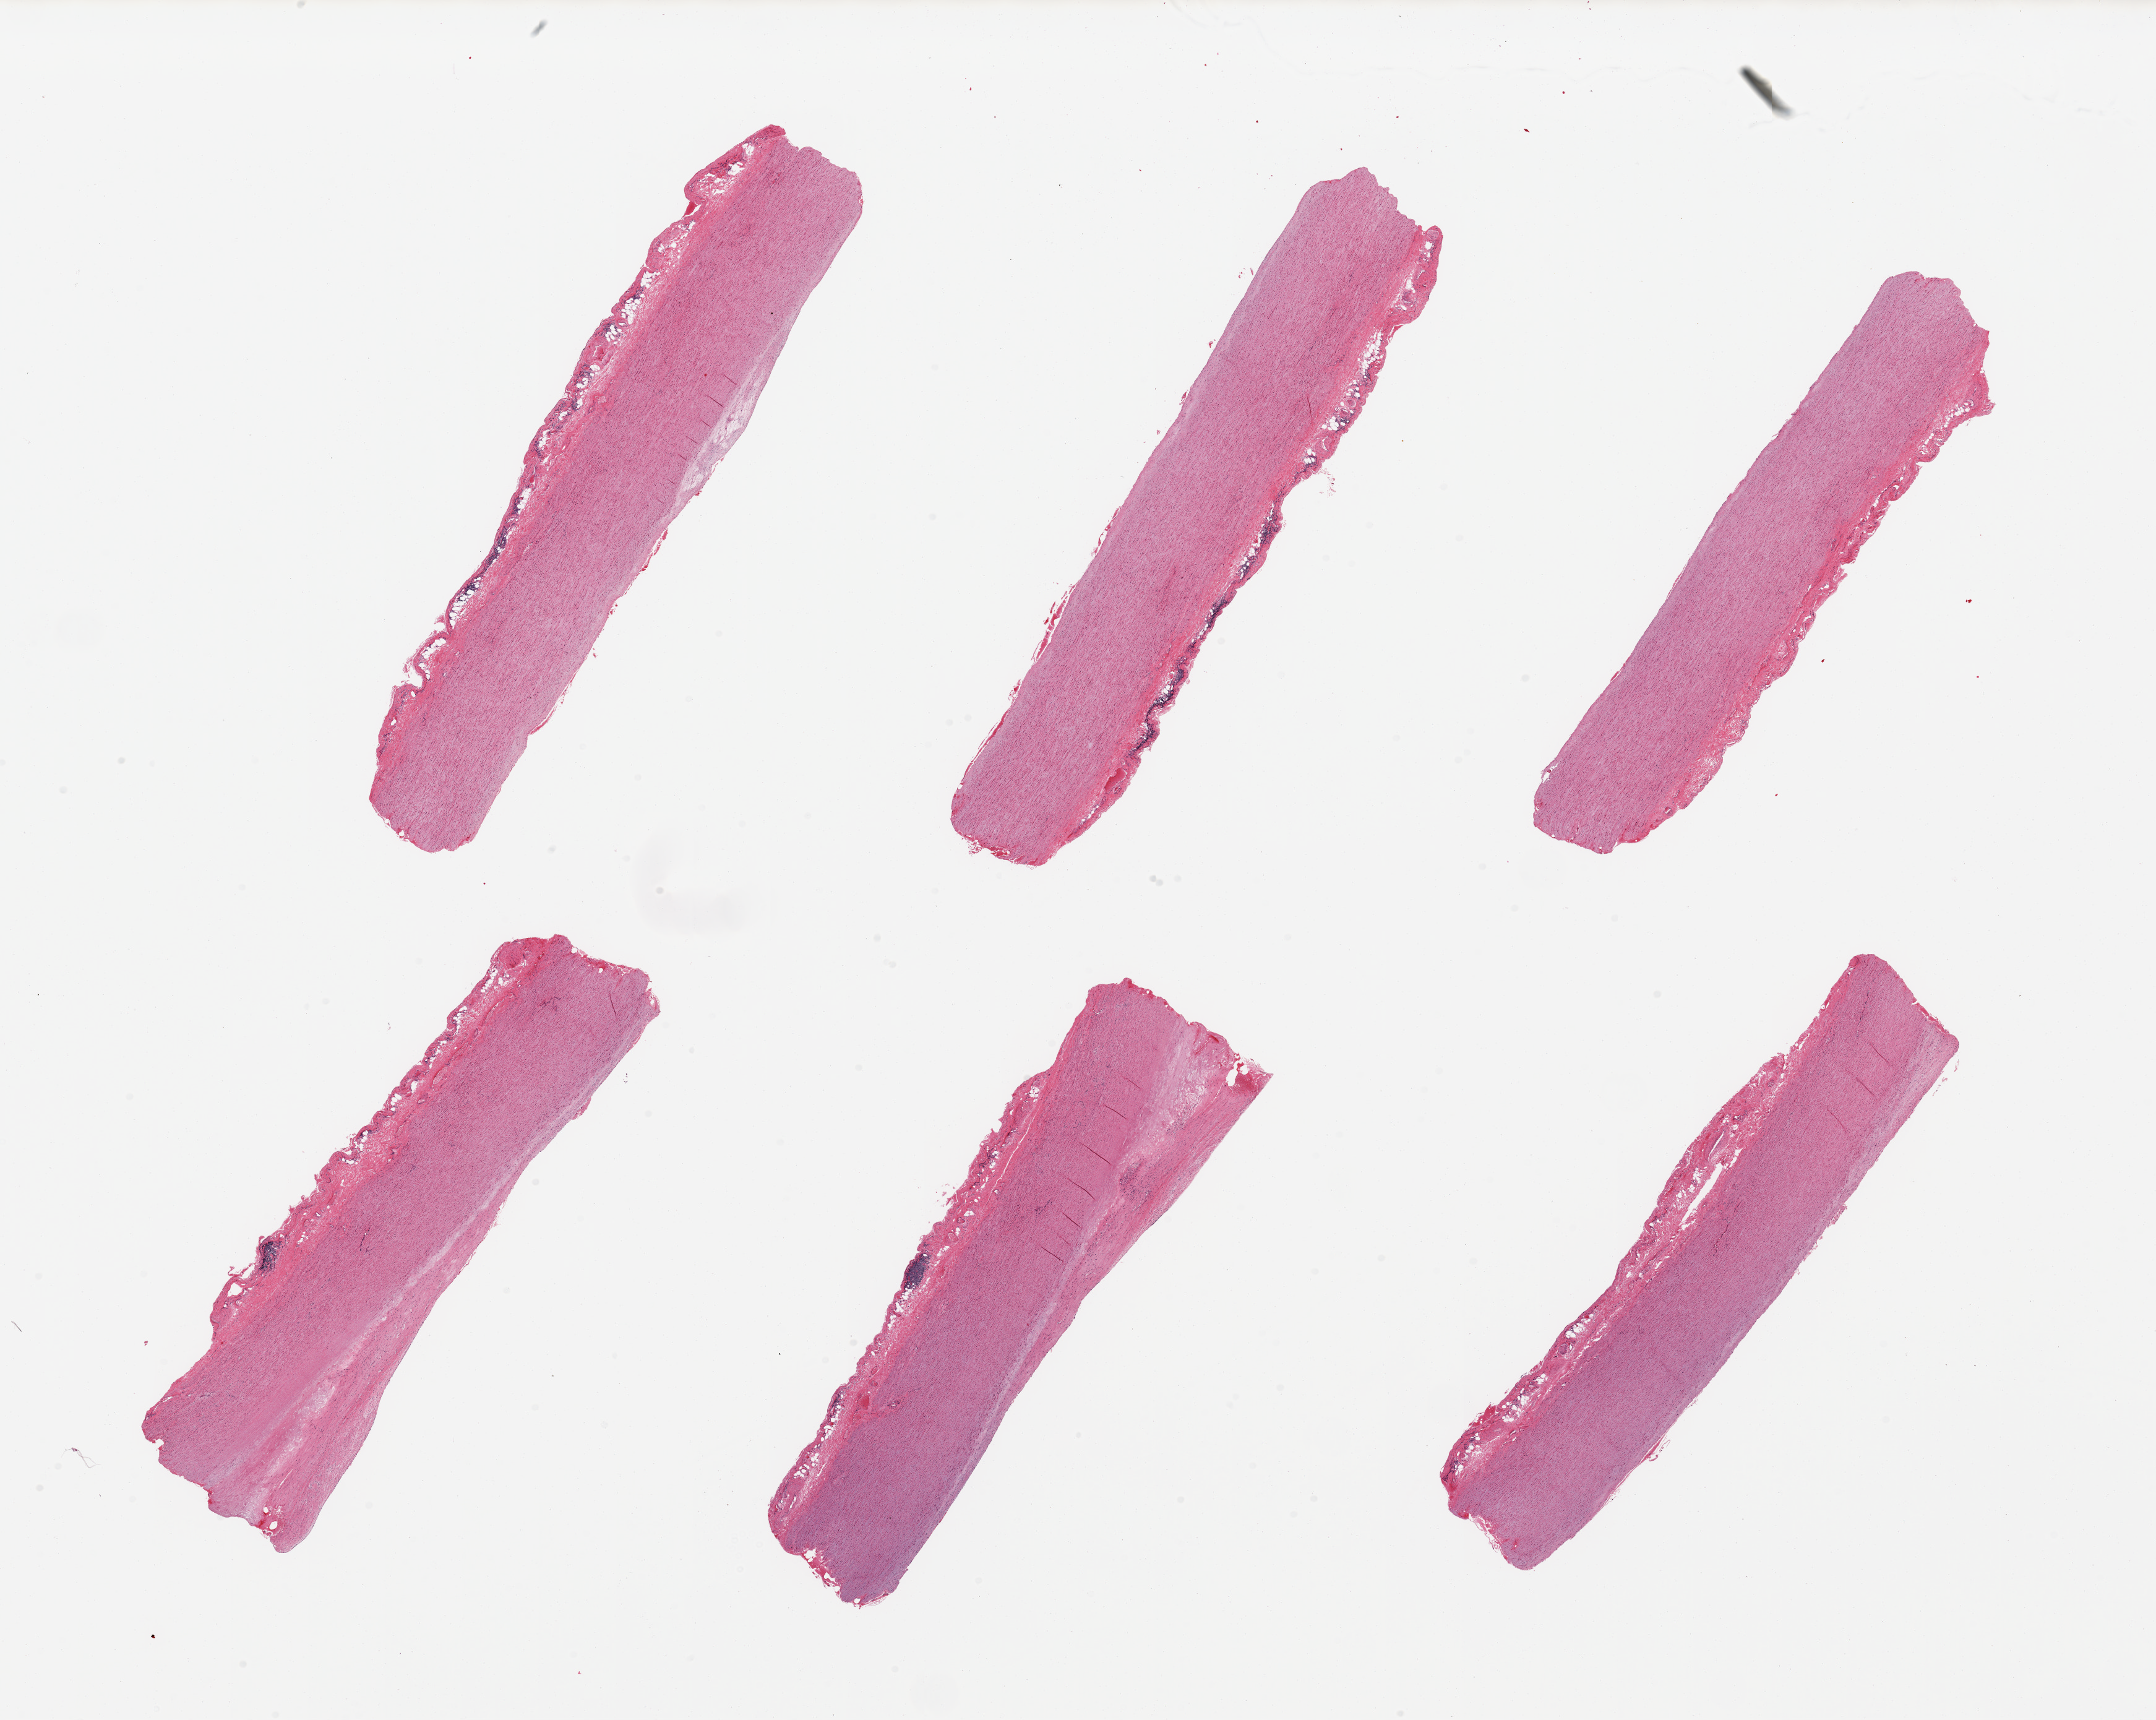
Whole-slide image, hematoxylin and eosin (H&E) stain, brightfield, a low-resolution overview of the entire scanned area, about 27.6 x 22.0 mm; PAXgene-fixed, paraffin-embedded tissue; target tissue: aorta; donor tissue sample.
- review note (as recorded): 6 pieces, atherosis up to ~1.5mm